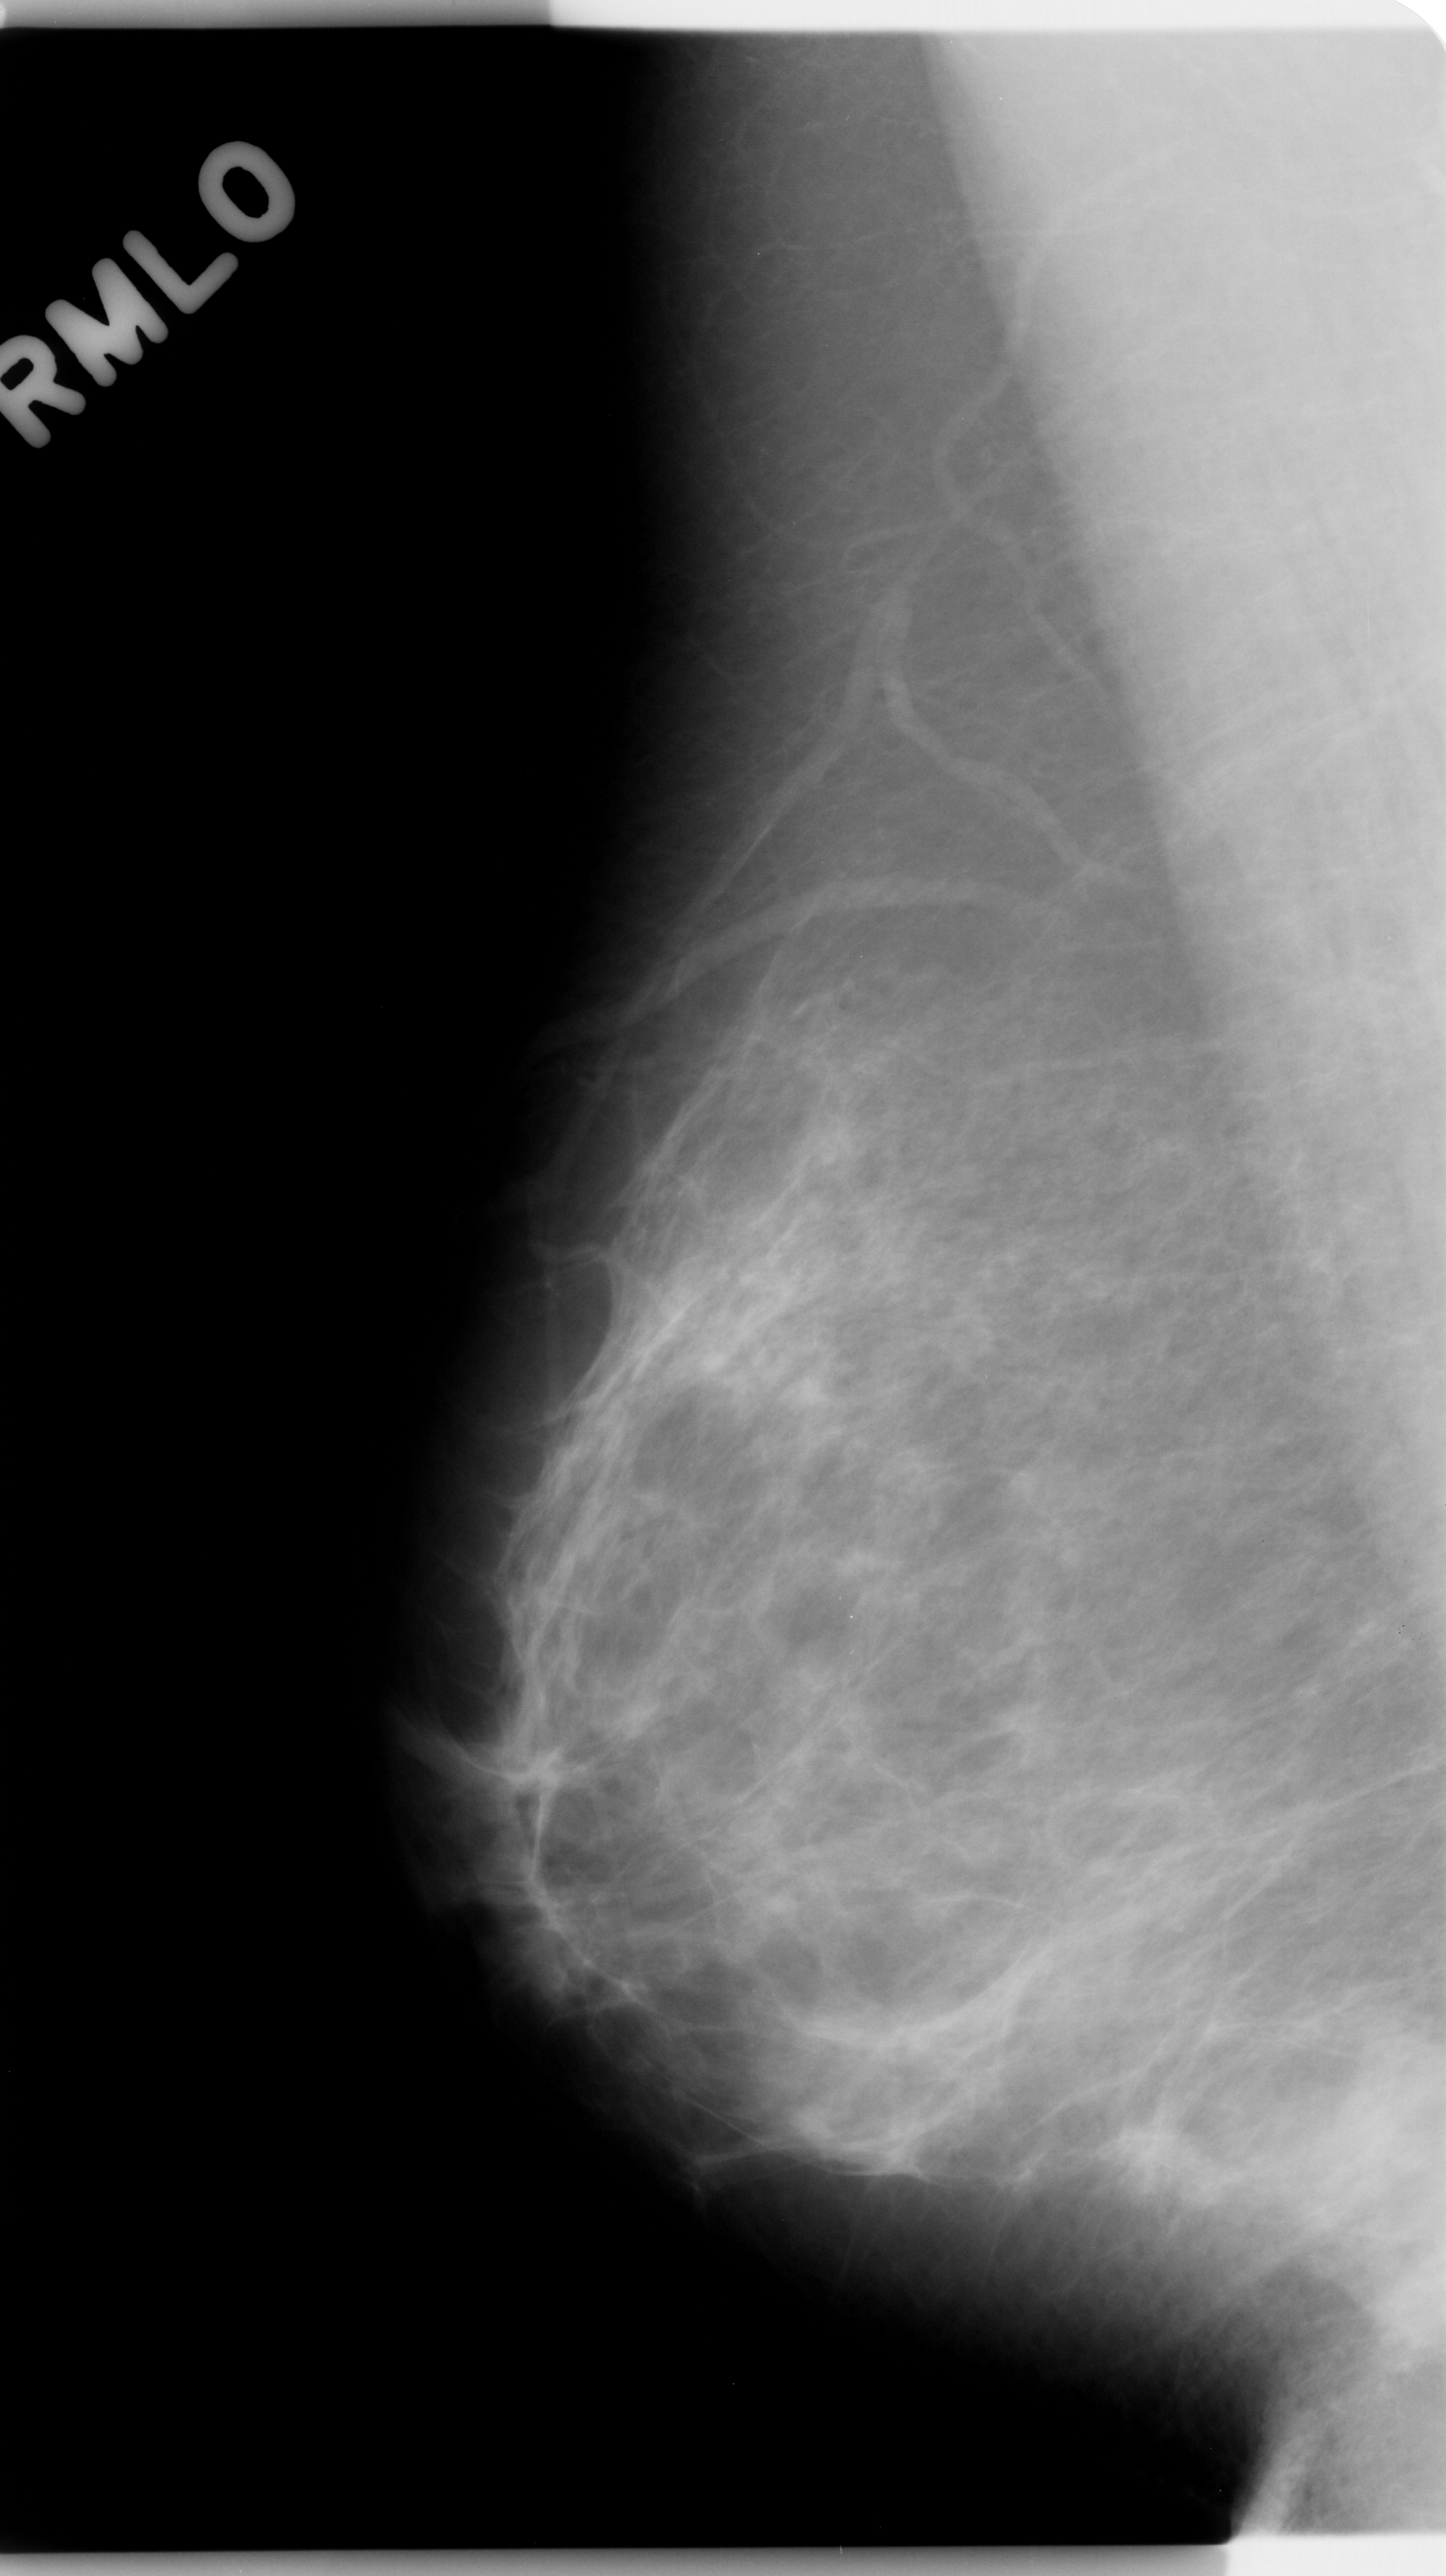
Scanned film-screen mammogram; right breast; mediolateral oblique (MLO) view; breast composition: scattered fibroglandular densities (BI-RADS density category 2 of 4); 1446 × 2576 image matrix.
Expert-marked regions of interest on this film, with their recorded descriptors:
- mass, shape irregular, margins ill defined; BI-RADS assessment category 4; pathology (as recorded): benign: bounding box [x1, y1, x2, y2] px = [1269, 2010, 1446, 2252]